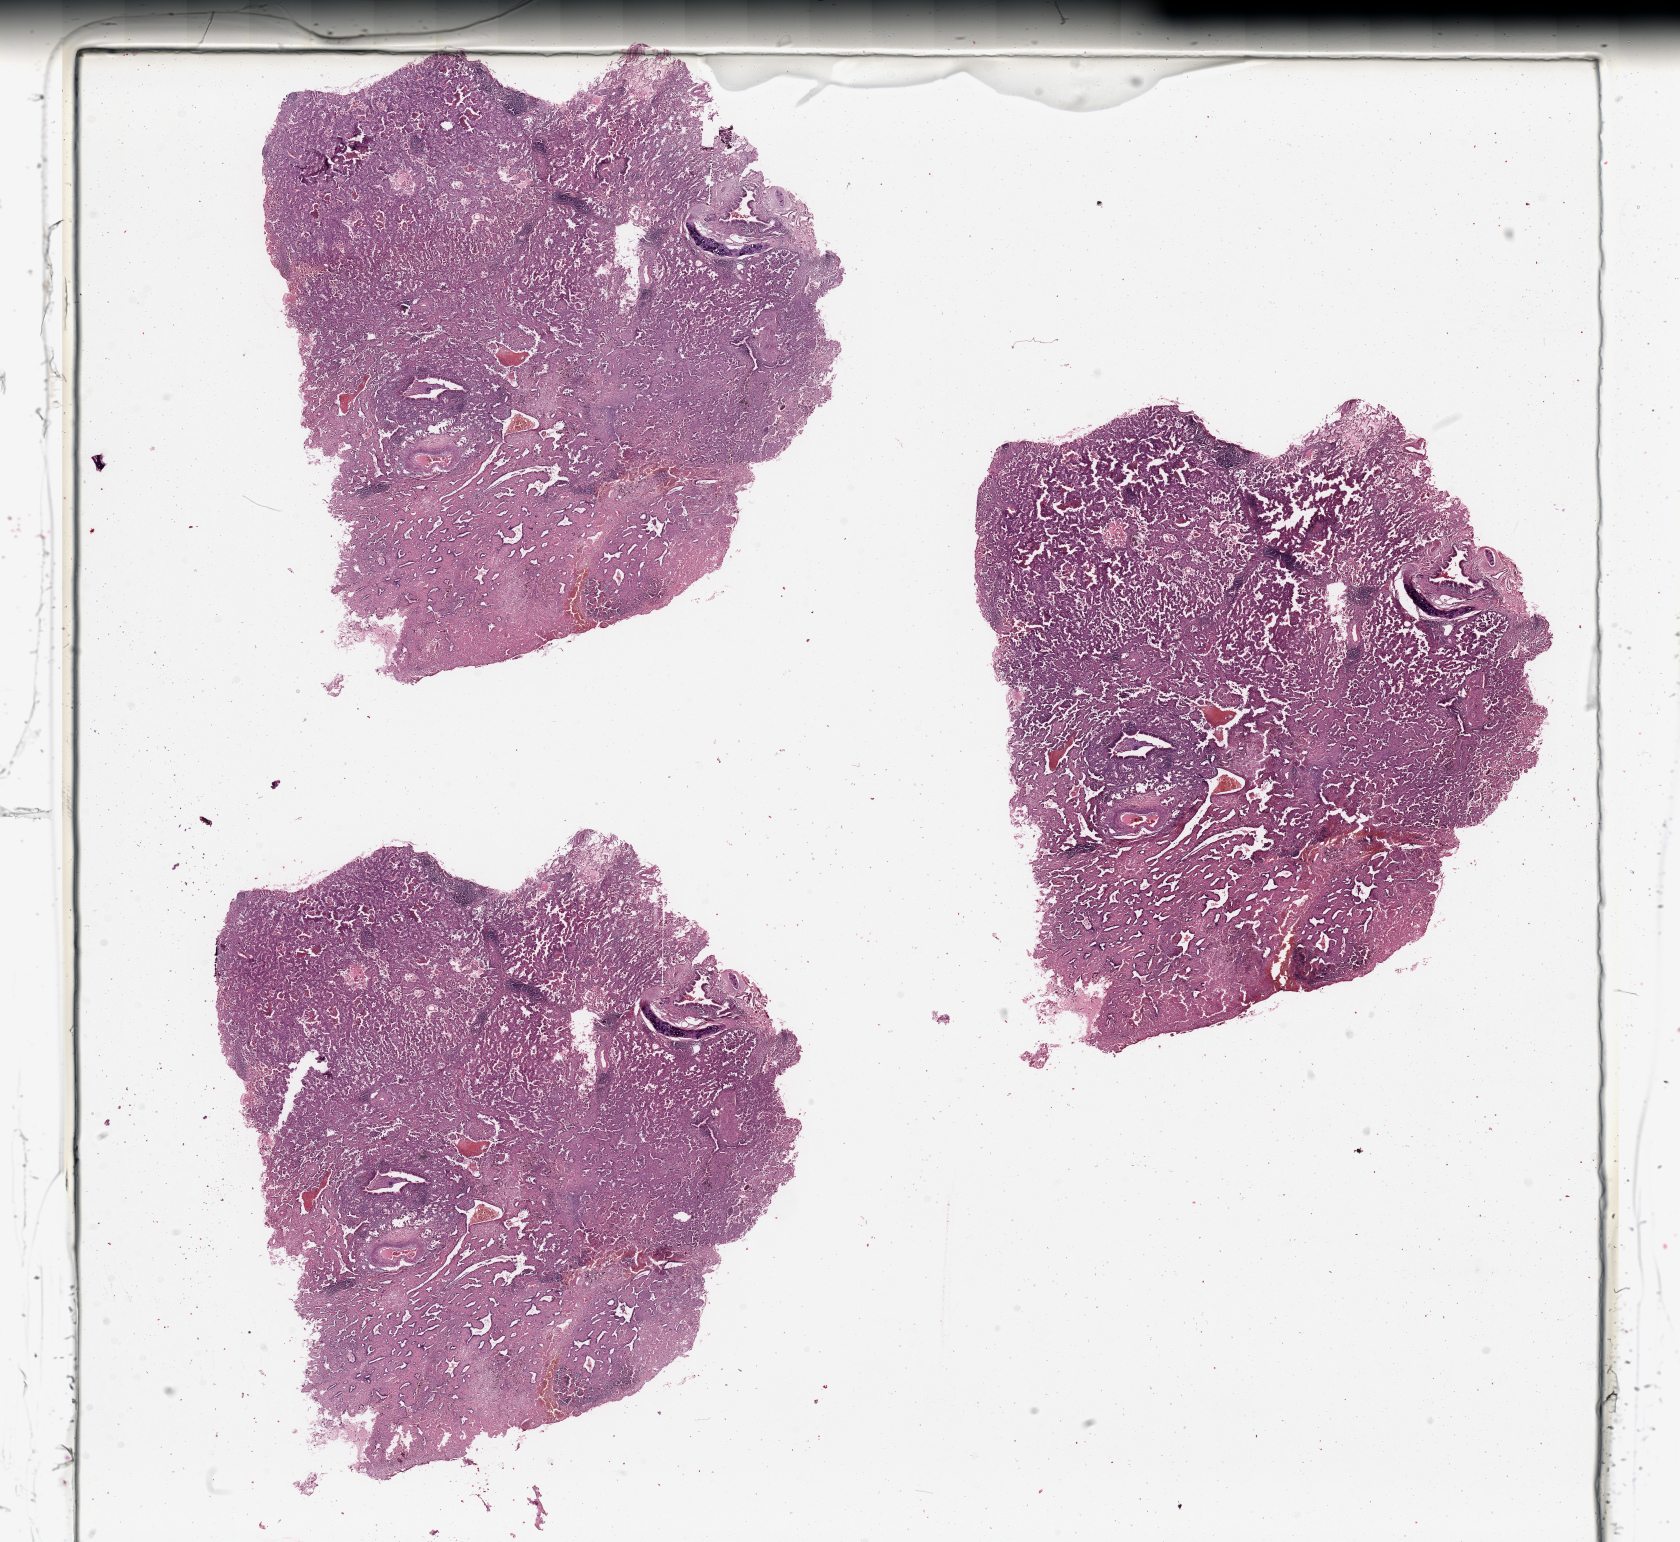
H&E whole-slide image — whole scanned area (about 26.6 x 24.4 mm, from a 20x scan) shown as a low-resolution overview; tumour tissue sample, sampled site: lung. 73-year-old female patient. Histologic grade: G2 (moderately differentiated). Pathologist review of this section (percent, as recorded): tumour nuclei 75%, necrosis 3%.
* primary tumour site (as recorded): right upper lobe
* AJCC pathologic stage: IB
* histologic diagnosis: Adenocarcinoma, NOS